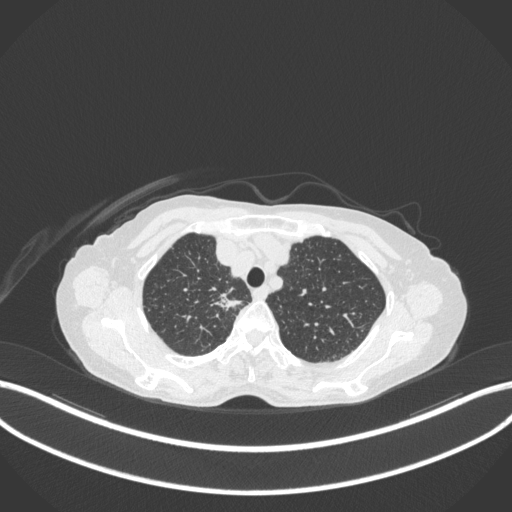
Chest CT, one axial slice; position 305 of 363 along the scan axis; 120 kVp; lung window (W 1500 / L -600 HU); 1 mm slice thickness; 512 × 512 image matrix, field of view 400 × 400 mm. Female patient, age 75 years. From the clinical record (not read from this slice): clinical TNM (as recorded): T1c N1 M1.
Structures marked on this image (bounding box drawn by a radiologist):
- lung tumour (recorded histology: adenocarcinoma): bounding box <211,288,247,316> (left, top, right, bottom; pixels)